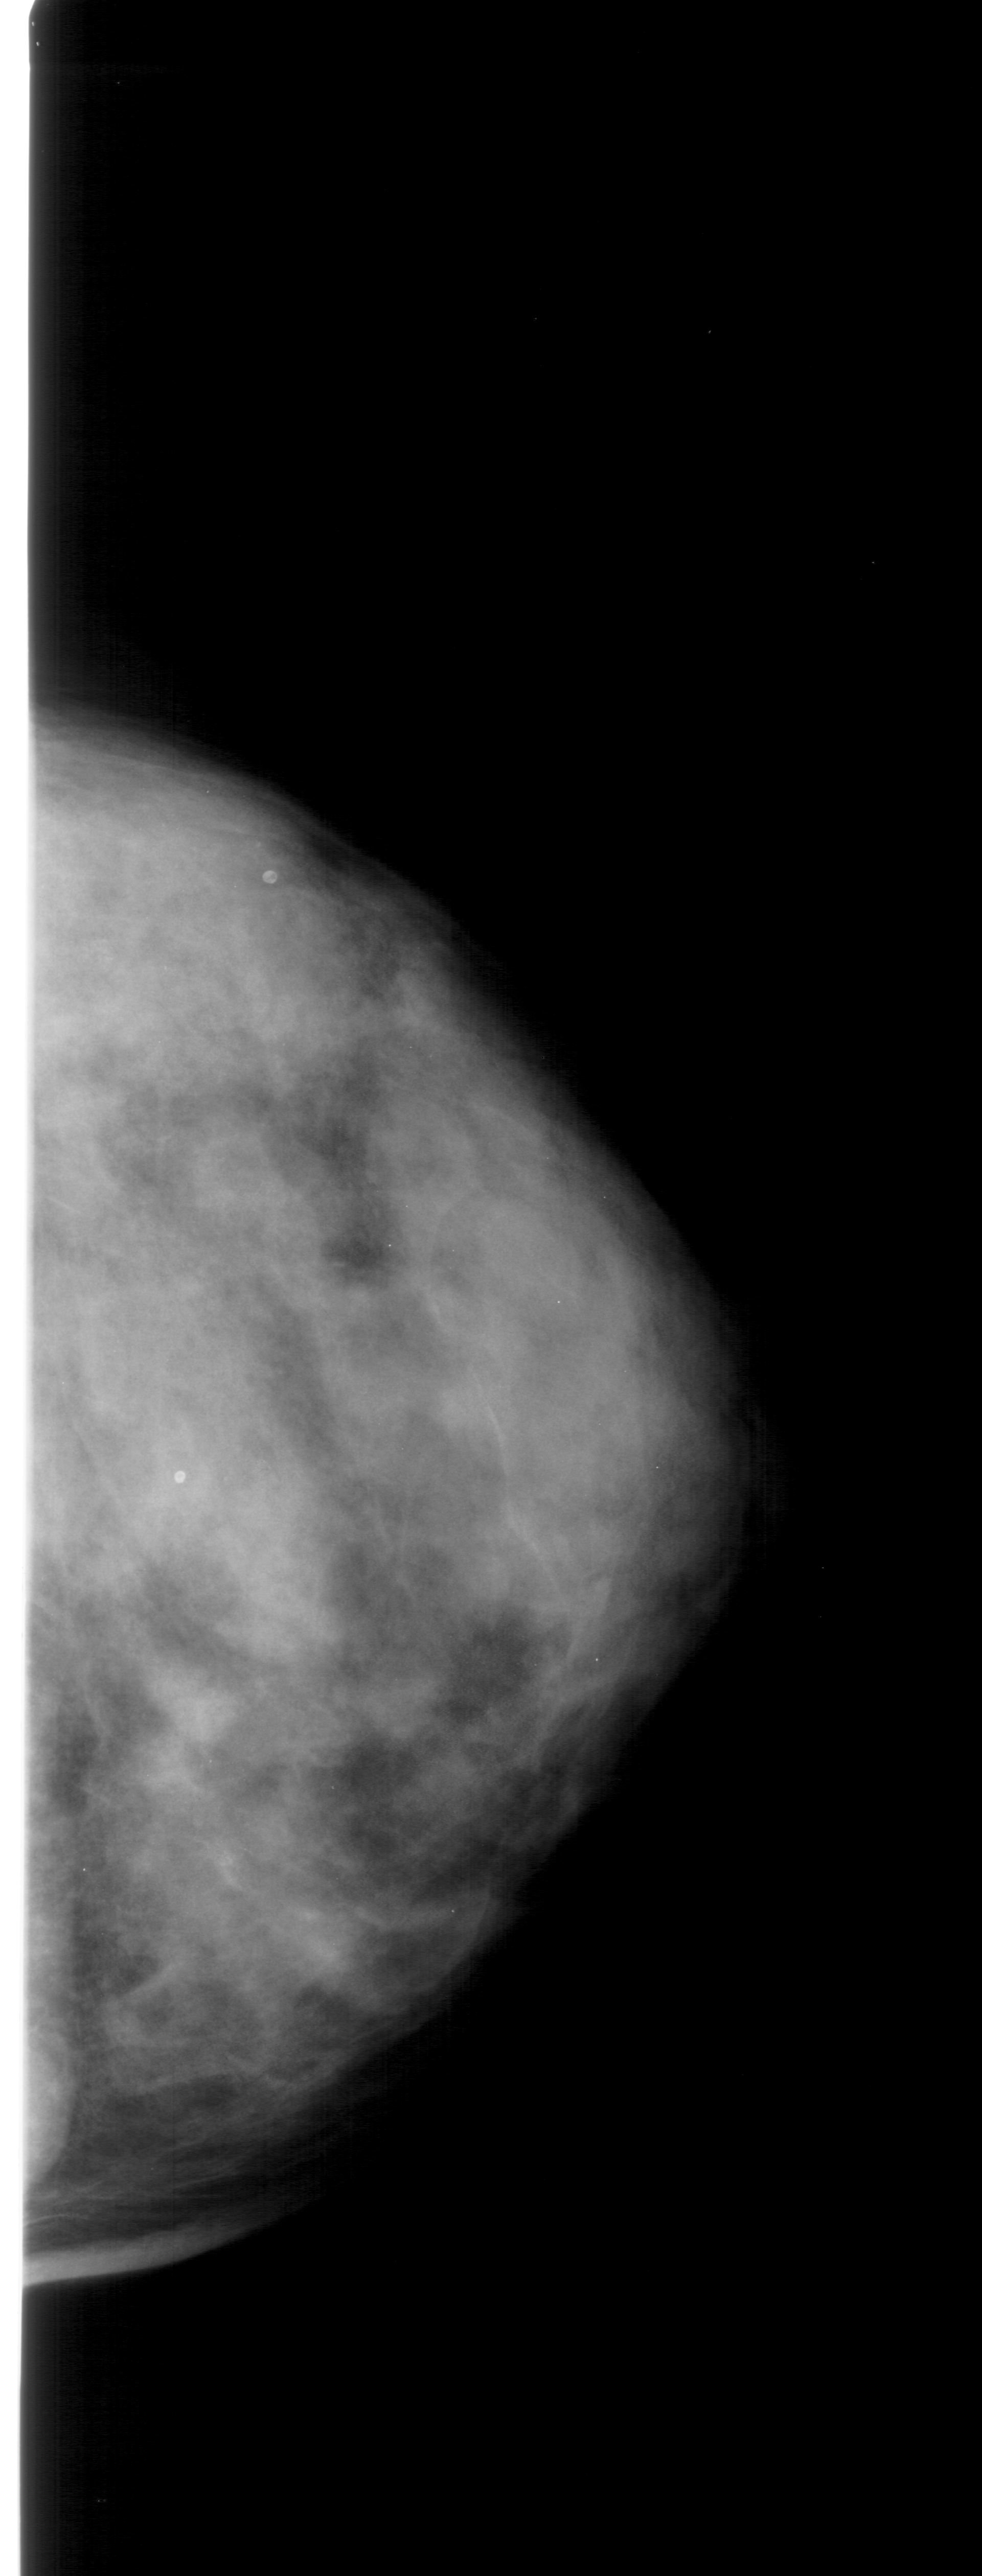
Mammogram (digitized film), right breast, craniocaudal (CC) view, BI-RADS breast density category 4 (scale 1–4).
Marked findings (only marked abnormalities are described; nothing is implied about the rest of the image): calcifications, morphology punctate, distribution segmental; BI-RADS assessment category 4; pathology (as recorded): benign.